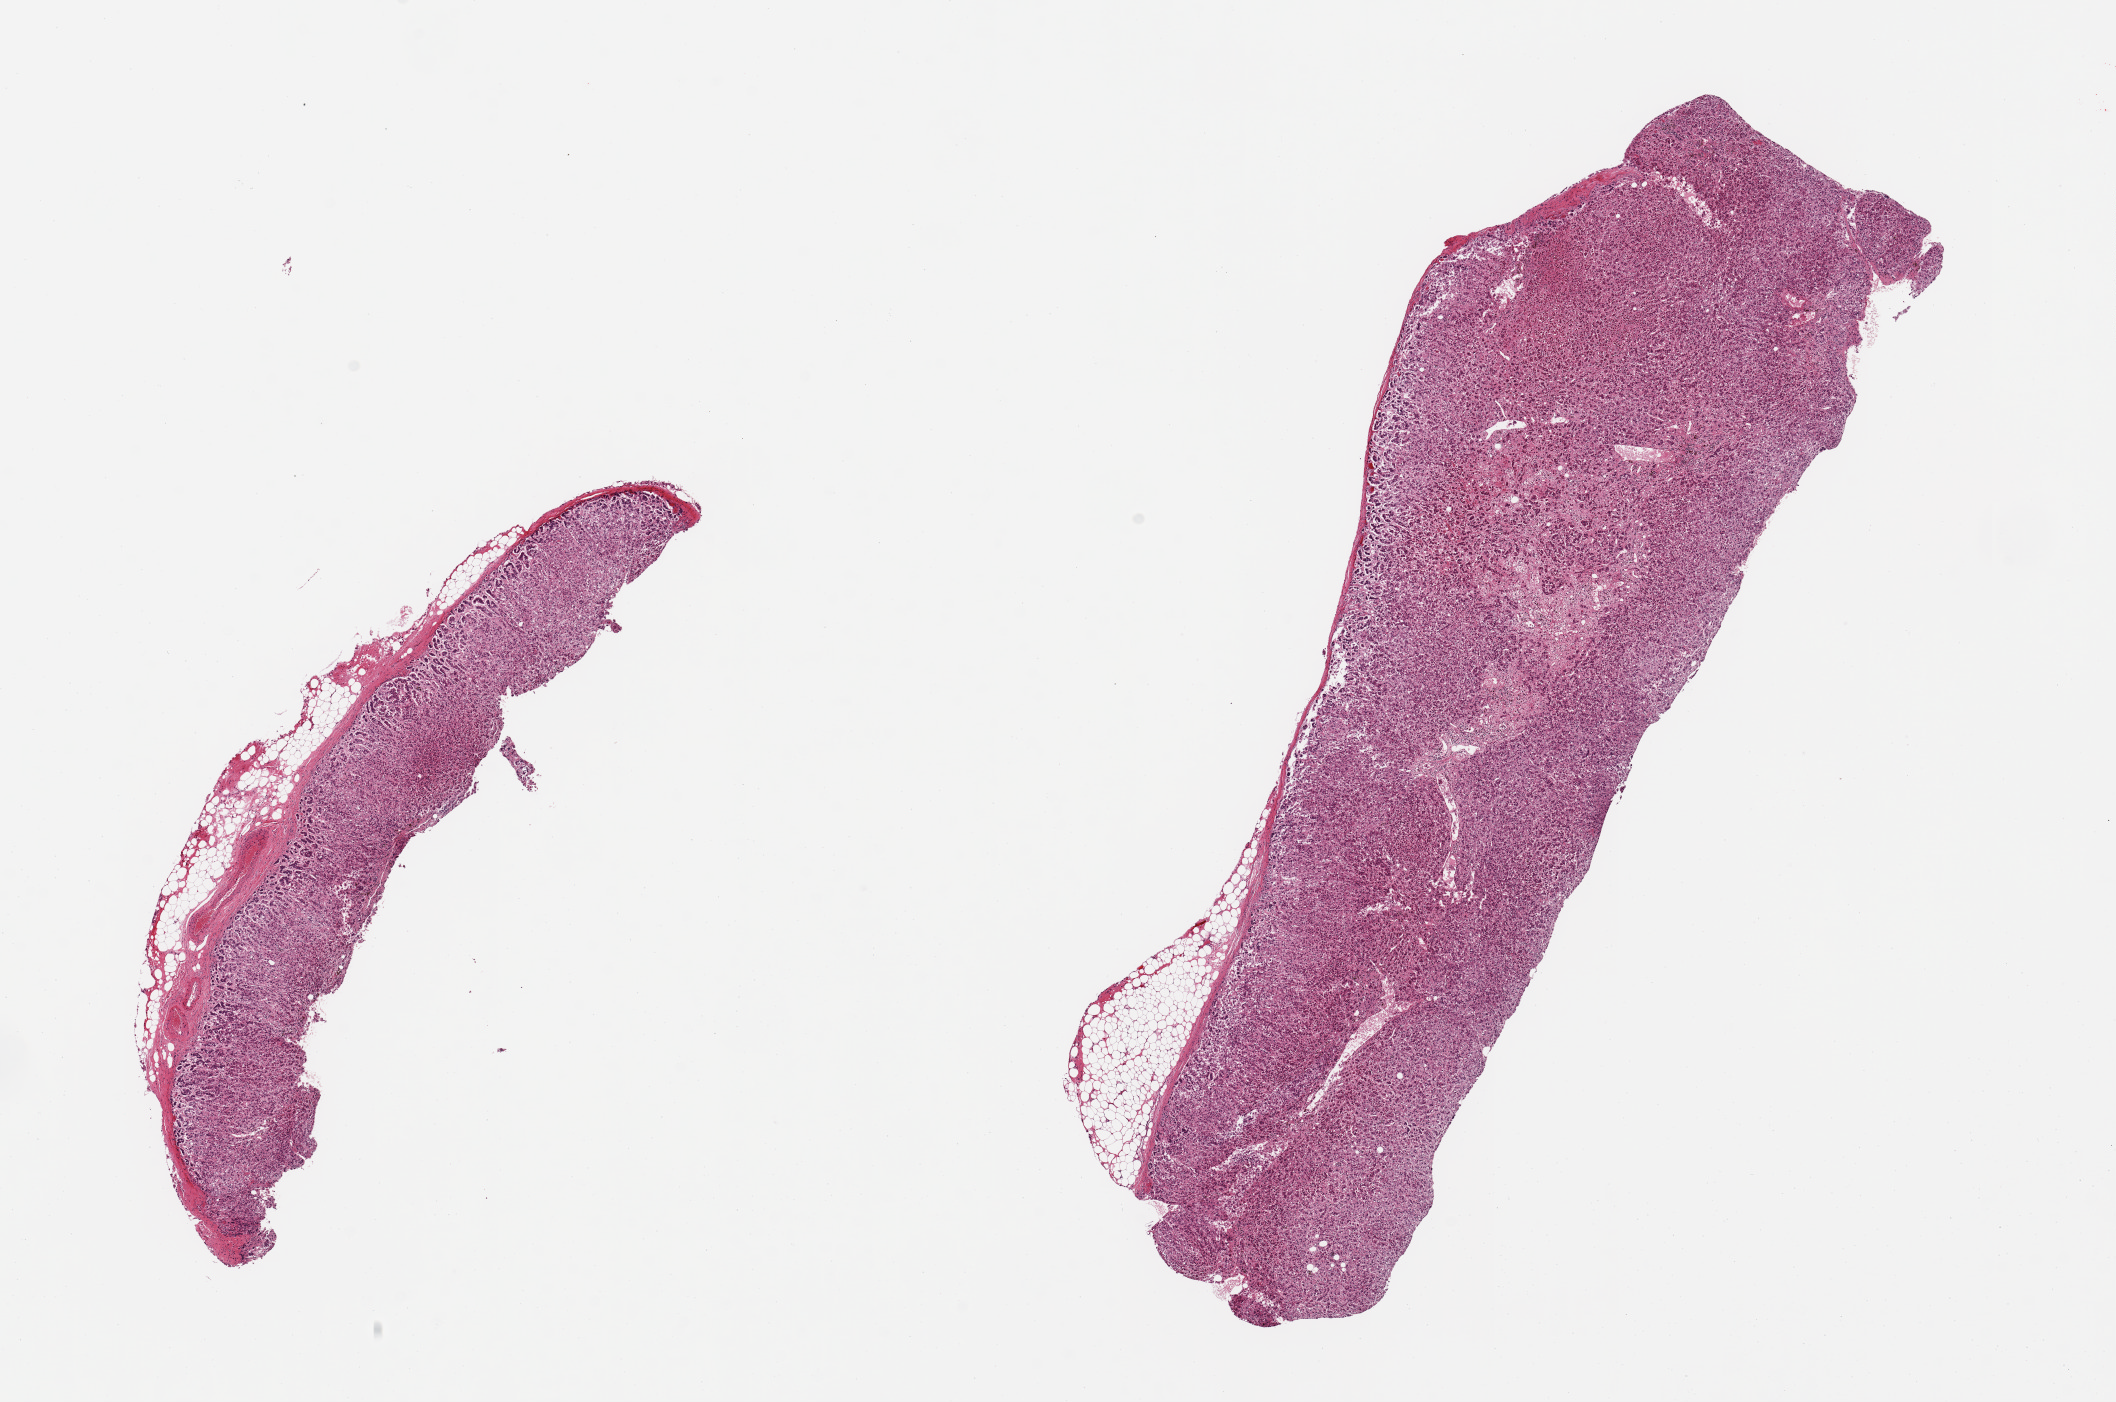
Haematoxylin and eosin whole-slide image, low-resolution overview of the scanned area, about 16.7 x 11.1 mm (from a 20x scan), PAXgene-fixed, paraffin-embedded tissue, section of adrenal gland (target tissue), donor tissue sample. Donor sex: male.
Review note (as recorded): 2 pieces, cortex, moderately advanced autolysis.